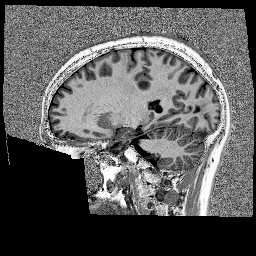
Brain MRI from a brain-tumour surgery series, one sagittal slice; 1 mm slice thickness; 256 × 256 image matrix, field of view 256 × 256 mm. From the clinical record (not read from this slice): histopathology: Glioblastoma; WHO grade: 4; IDH mutation: no.
Structures marked on this image (outlined manually by an expert reader):
- tumour: bounding box (x1, y1, x2, y2) in pixels: (131, 67, 149, 86)